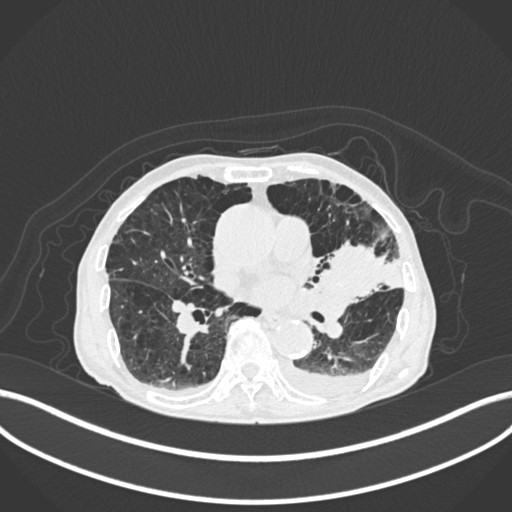
Chest CT, one axial slice. Slice 105 of 400 in the series (ordered by position). Lung window (W 1500 / L -600 HU). 512 × 512 image matrix, field of view 400 × 400 mm. Patient: male, 90 years or older. Case-level facts recorded for this patient, not image findings: clinical TNM (as recorded): T2b N1 M0.
Outlined on this slice (bounding box drawn by a radiologist):
- lung tumour (recorded histology: squamous cell carcinoma): bounding box [x1, y1, x2, y2] px = [325, 240, 390, 305]